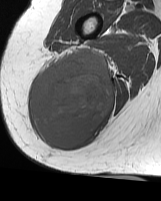
MRI of an extremity soft-tissue mass, one axial slice. Position 27 of 70 along the scan axis. MR volume resampled by the dataset authors to the PET/CT grid (not the native acquisition matrix). 3.27 mm slice thickness. 161 × 201 image matrix, field of view 157 × 196 mm. Female patient. From the clinical record (not read from this slice): histological type: synovial sarcoma; grade: intermediate; site of the primary tumour: right buttock.
Annotated regions visible in this slice (expert contour drawn on MRI and transferred to this co-registered scan by the dataset authors):
- gross tumour volume including surrounding oedema: box from (x=31, y=51) to (x=114, y=149) px
- gross tumour volume (mass): (x=31, y=51)–(x=114, y=149)